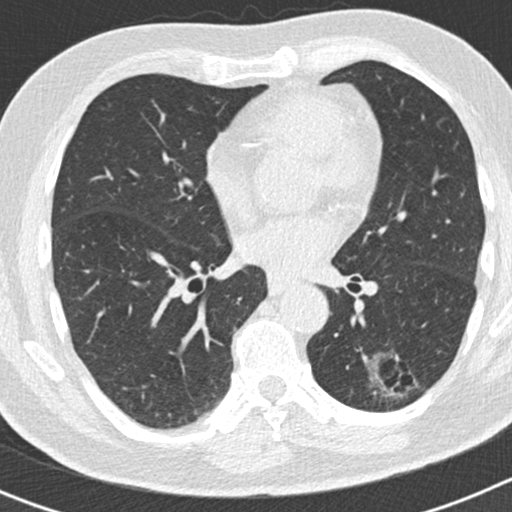
Axial slice from a low-dose chest CT screening exam, second annual screen, lung window (W 1500 / L -600 HU), standard (soft-tissue) reconstruction kernel (B30f). Male, age 66 years at enrolment. Former smoker at enrolment.
Expert reader's lesion annotation, box from (x=351, y=336) to (x=413, y=406) px. Screening reader's record for this exam (one nodule recorded; not confirmed to be the boxed lesion): non-calcified nodule or mass ≥4 mm, left lower lobe, 50 × 33 mm, smooth margins, pre-existing on the prior screen: yes; interval growth: yes. Later outcome: lung cancer diagnosed 440 days after this screen — adenocarcinoma, NOS, left lower lobe, poorly differentiated (G3), stage IB (AJCC 6th edition), 38 mm at pathology.